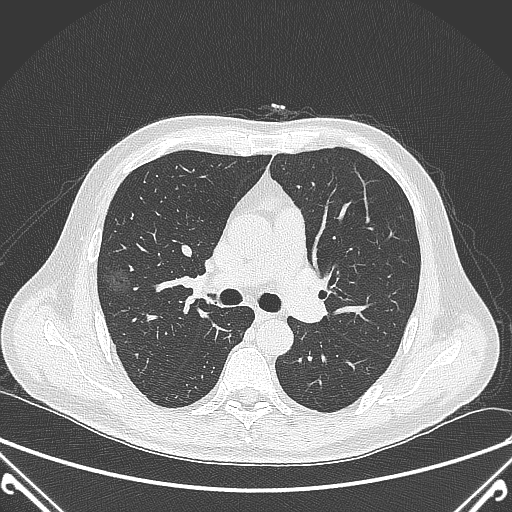
Chest CT, one axial slice. Position 227 of 360 along the scan axis. 120 kVp. Lung window (W 1500 / L -600 HU). 1 mm slice thickness. 512 × 512 image matrix, field of view 380 × 380 mm. Male patient, age 64 years. Case-level facts recorded for this patient, not image findings: clinical TNM (as recorded): T1c N0 M0.
Annotated regions visible in this slice (rectangle marked by the reading radiologist):
- lung tumour (recorded histology: adenocarcinoma): box from (x=108, y=256) to (x=144, y=300) px